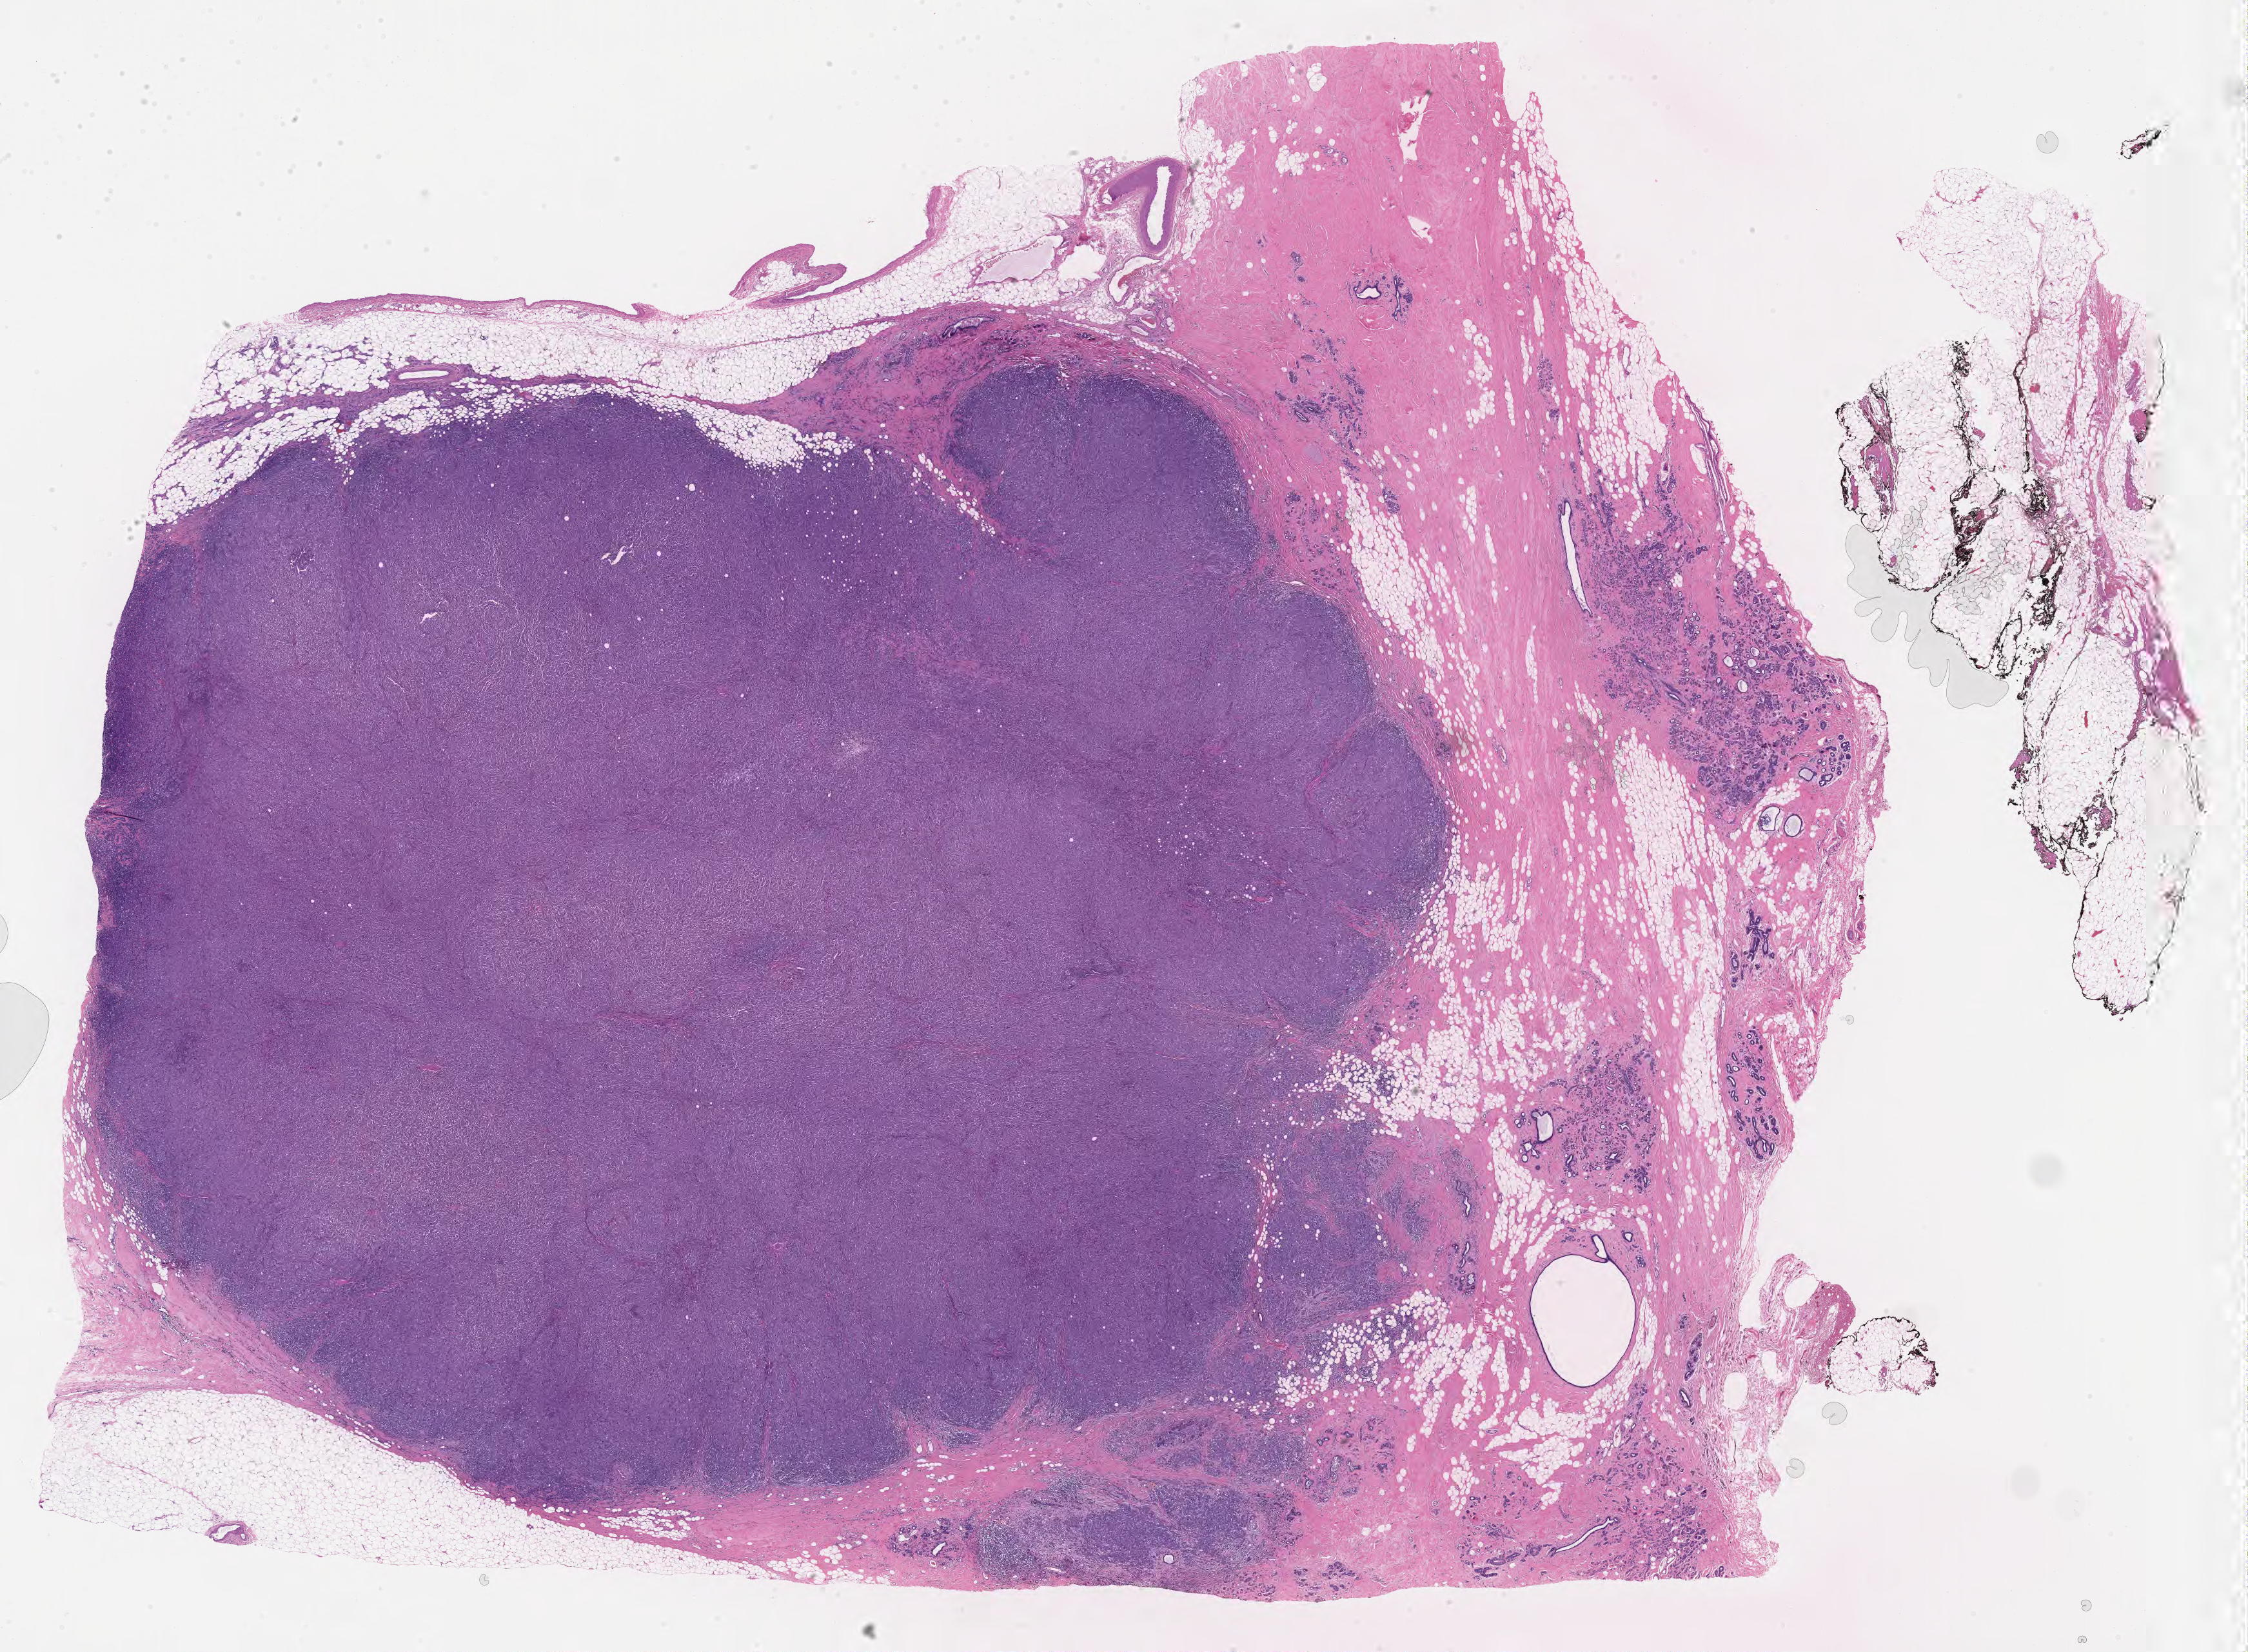
Digitized haematoxylin and eosin-stained section — a low-resolution overview of the entire scanned area, about 28.1 x 20.7 mm; FFPE section; specimen: primary tumor; site: breast (right). Female, age 43 years at initial diagnosis. Tumor grade: G3 (poorly differentiated). Composition of this section per pathologist review: tumor cells 85%, tumor nuclei 85%, stromal cells 12%, necrosis 0%, normal cells 3%. Inflammatory infiltration, as recorded: lymphocyte infiltration 4%, monocyte infiltration 1%, neutrophil infiltration 3%.
• section: top of the tissue portion
• diagnosis: Lobular carcinoma, NOS
• AJCC pathologic stage: Stage IIA